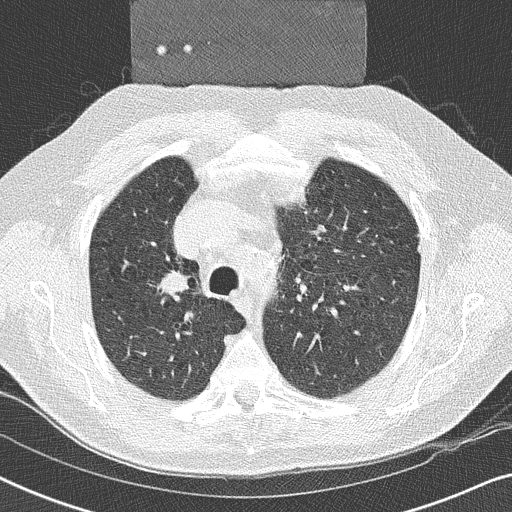
Low-dose screening chest CT, one axial slice; slice 178 of 252 in the series (ordered by position); reconstruction kernel B50f; lung window (W 1500 / L -600 HU); 2 mm slice thickness; 512 × 512 image matrix.
Annotated regions visible in this slice (expert manual segmentation):
- lesion 1 (tumor, upper lobe of right lung): bounding box [x1, y1, x2, y2] px = [162, 273, 188, 293]